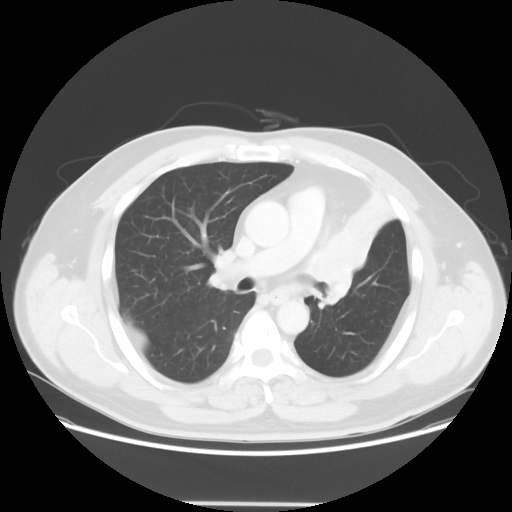
Chest CT, one axial slice; slice 37 of 62 in the series (ordered by position); reconstruction kernel STANDARD; 120 kVp; lung window (W 1500 / L -600 HU); 512 × 512 image matrix, field of view 403 × 403 mm. Patient: male, 49 years. From the clinical record (not read from this slice): clinical TNM (as recorded): T3 N3 M1c.
Annotated regions visible in this slice (rectangle marked by the reading radiologist):
- lung tumour (recorded histology: squamous cell carcinoma): bounding box <304,208,372,307> (left, top, right, bottom; pixels)